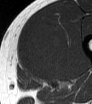
MRI of an extremity soft-tissue mass, one axial slice. MR volume resampled by the dataset authors to the PET/CT grid (not the native acquisition matrix). 3.27 mm slice thickness. 92 × 104 image matrix, field of view 90 × 102 mm. Male patient. From the clinical record (not read from this slice): histological type: mixoid liposarcoma; grade: low; site of the primary tumour: left thigh.
Structures marked on this image (expert contour drawn on MRI and transferred to this co-registered scan by the dataset authors):
- gross tumour volume (mass): bounding box [x1, y1, x2, y2] px = [21, 22, 70, 82]